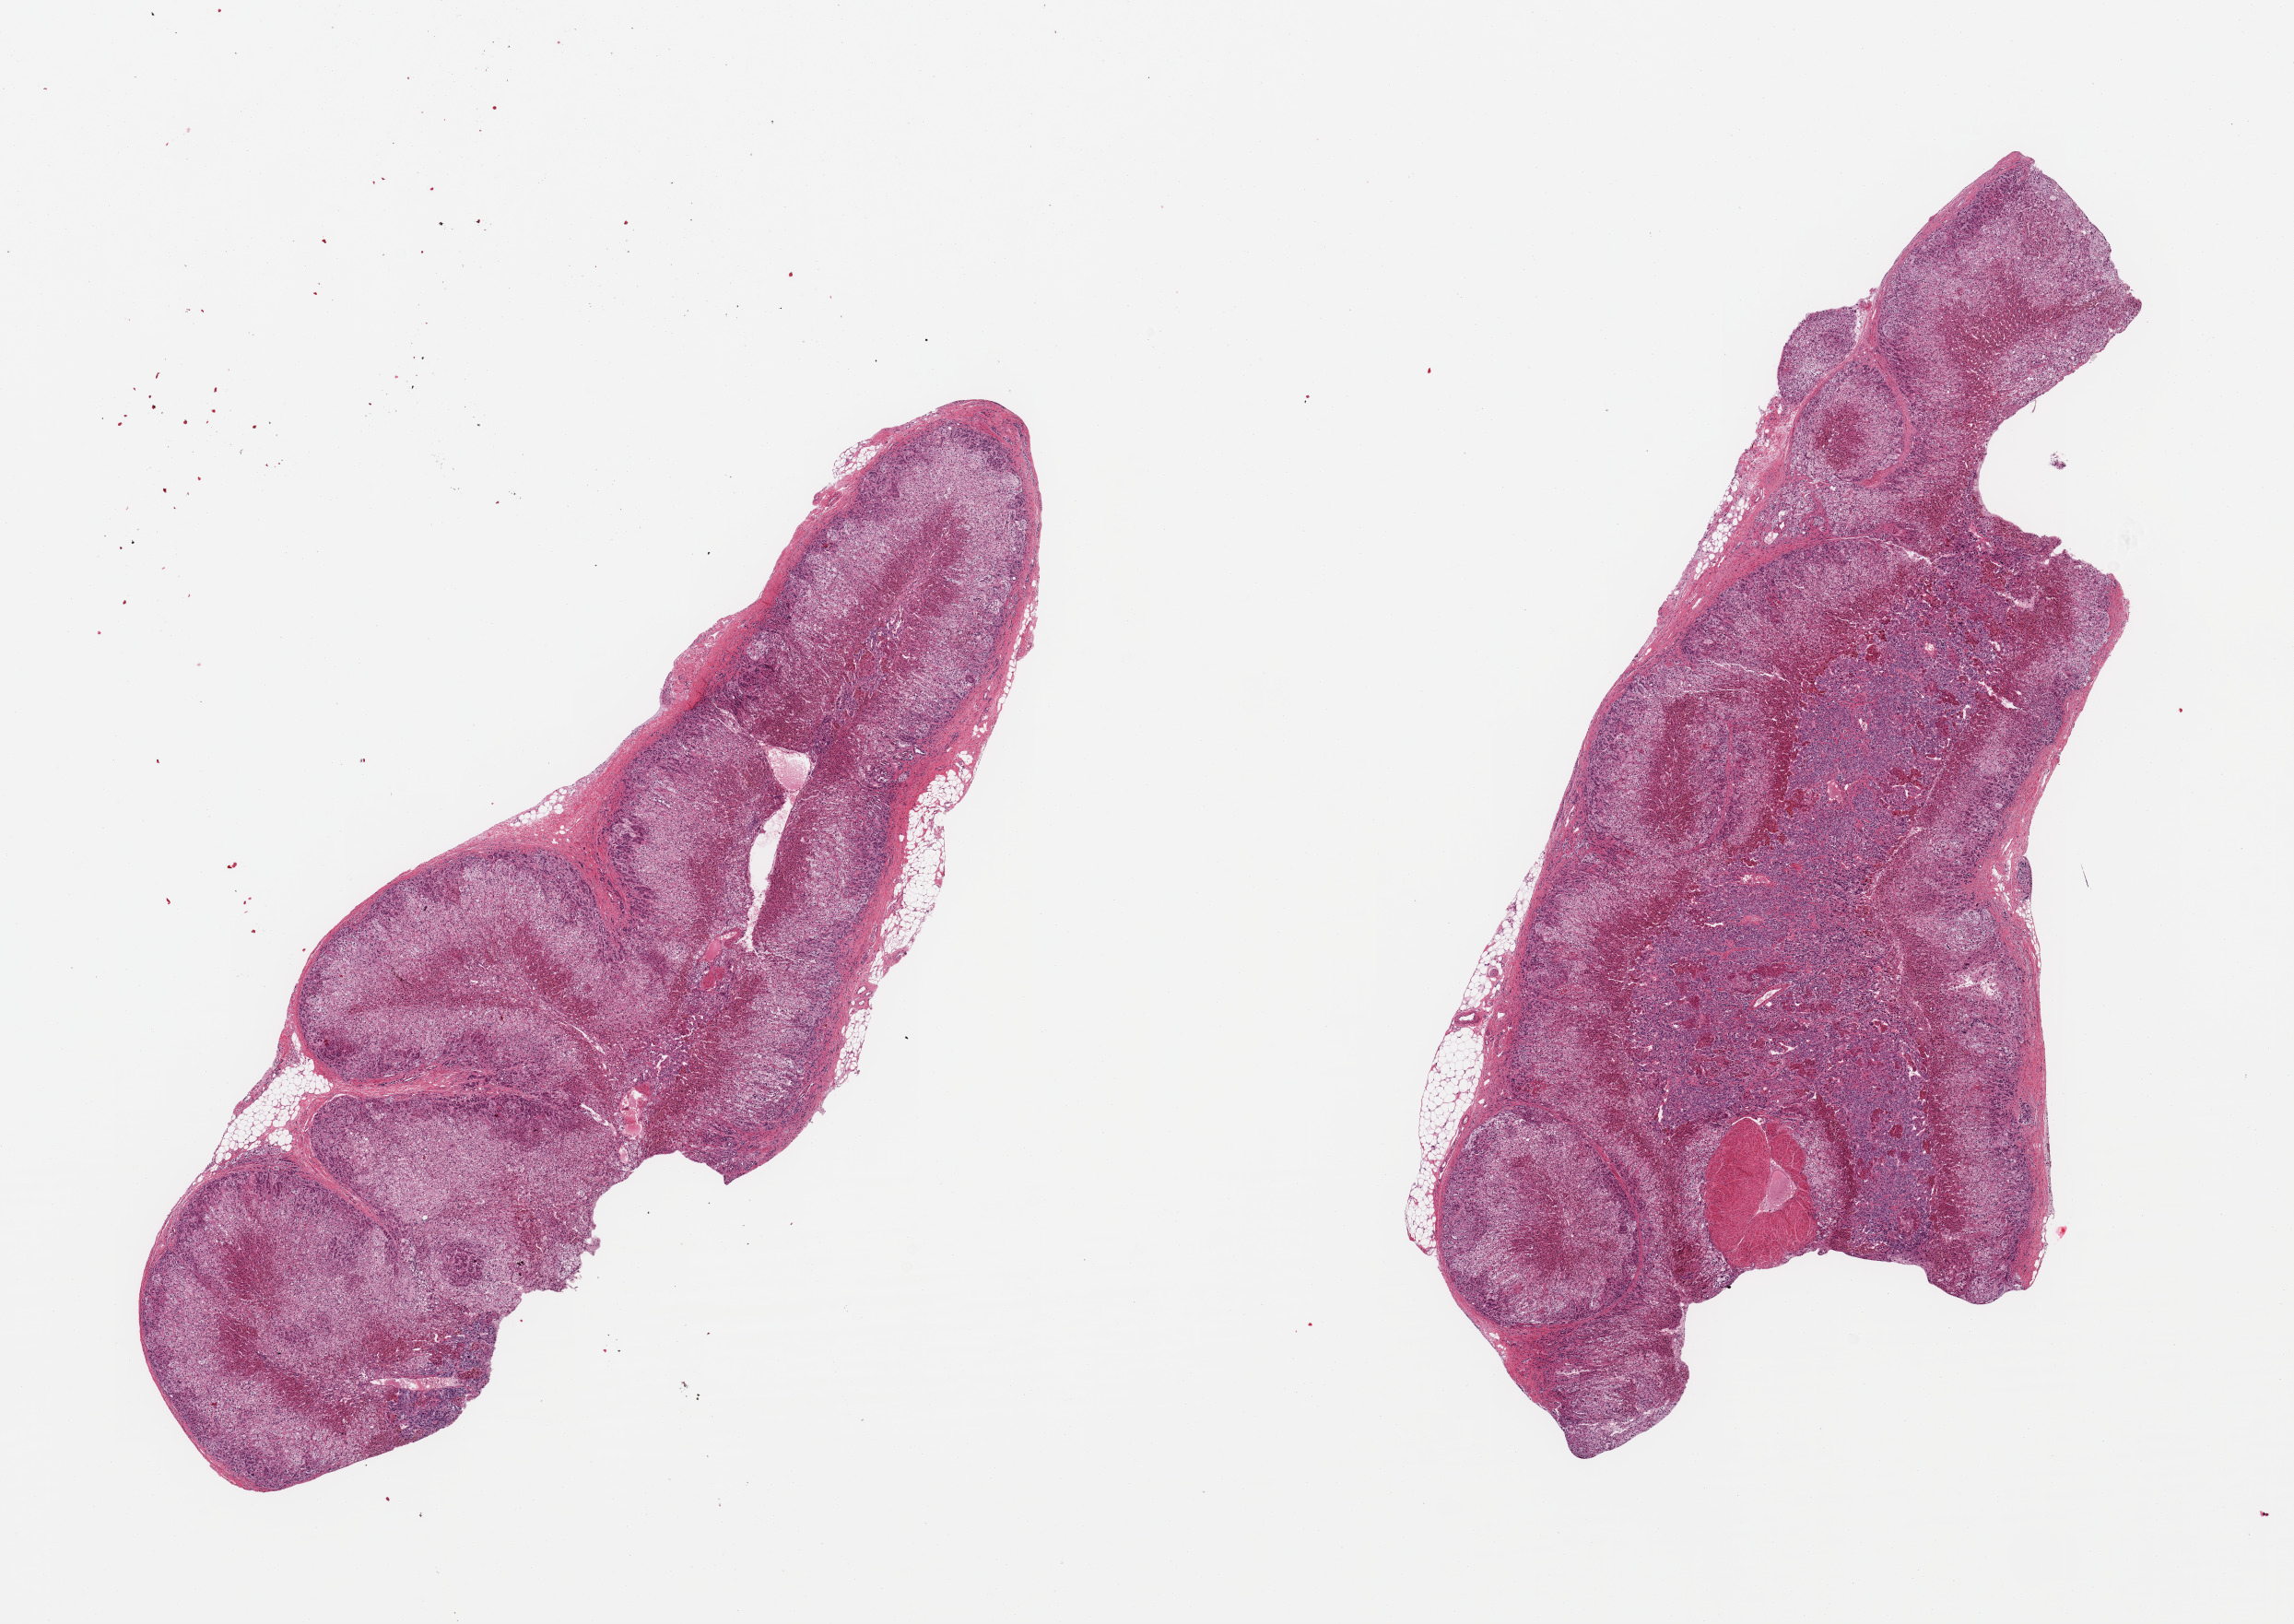
Digitized hematoxylin and eosin (H&E)-stained section — low-resolution overview of the scanned area, about 19.7 x 13.9 mm (acquisition: 20x scan), PAXgene-fixed paraffin-embedded (PFPE) section, section of adrenal gland (target tissue), tissue donor sample. Male donor.
Reviewer comment on this tissue sample: 2 pieces; adrenal cortex and ~5% attached external fat.